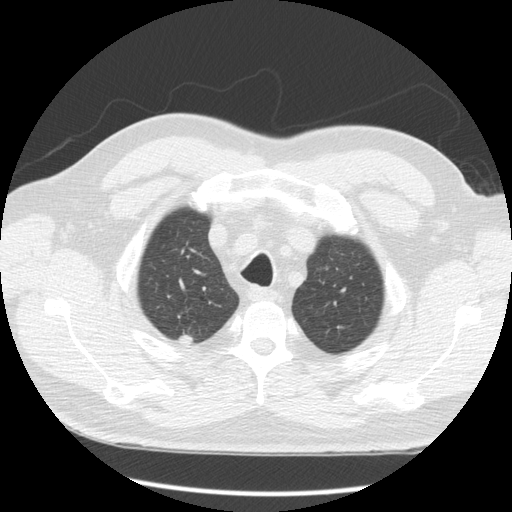
Low-dose screening chest CT, one axial slice; slice 145 of 163 in the series (ordered by position); reconstruction kernel STANDARD; 120 kVp; lung window (W 1500 / L -600 HU); 2.5 mm slice thickness; 512 × 512 image matrix, field of view 360 × 360 mm.
Structures marked on this image (outlined manually by an expert reader):
- lesion 1 (tumor, upper lobe of right lung): box from (x=179, y=332) to (x=194, y=343) px